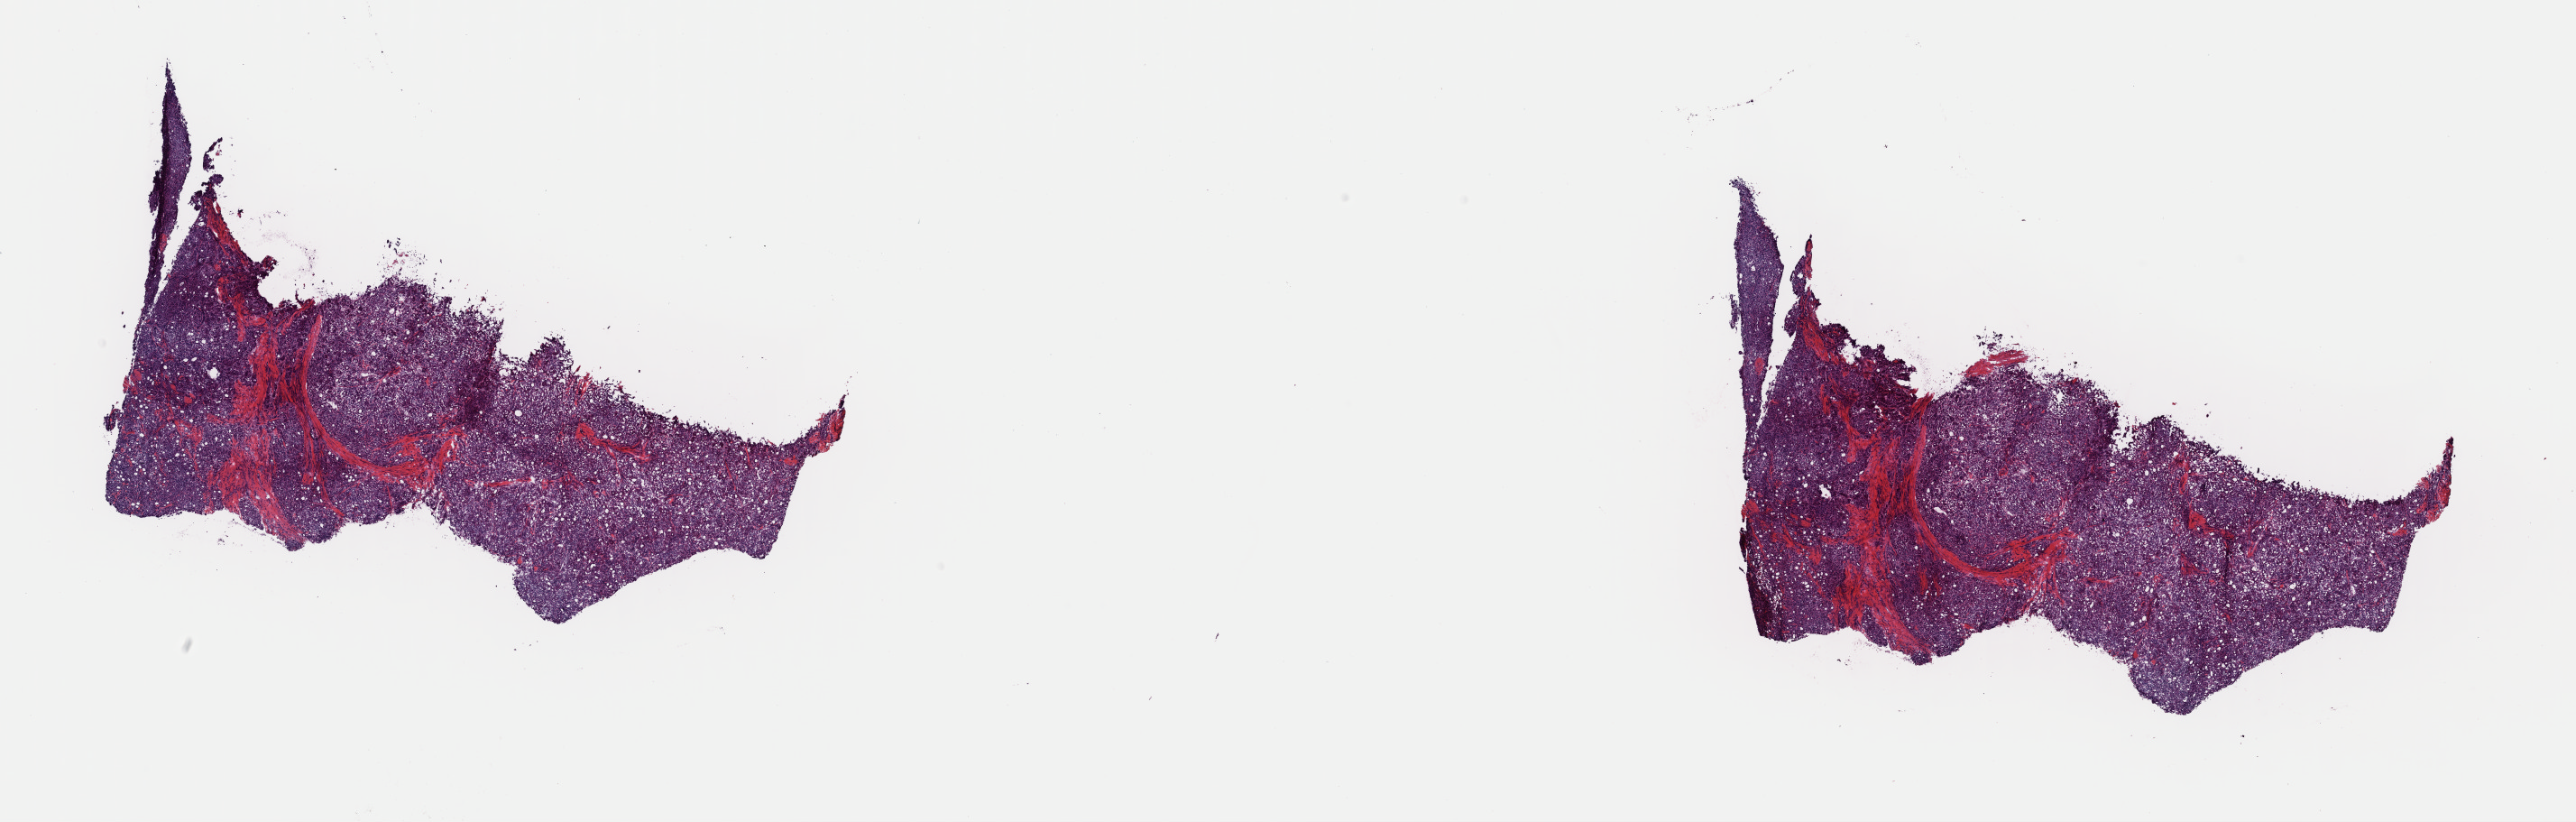
Whole-slide histology image, H&E, low-resolution overview of the scanned area, about 22.6 x 7.2 mm (from a 40x scan). Frozen section. Primary tumour sample from the thyroid. Female, age 46 years at initial diagnosis. Slide review estimates, as recorded: tumour cells 90%, tumour nuclei 90%, normal cells 0%, stromal cells 10%, necrosis 0%. Infiltration values recorded for this section: lymphocyte infiltration 15%, monocyte infiltration 0%, neutrophil infiltration 0%.
Lymph nodes positive (case pathology): 0 of 4 examined. Laterality: left. TNM: T1a N0 M0. Diagnosis: Papillary adenocarcinoma, NOS (thyroid gland). AJCC pathologic stage: I (7th edition).